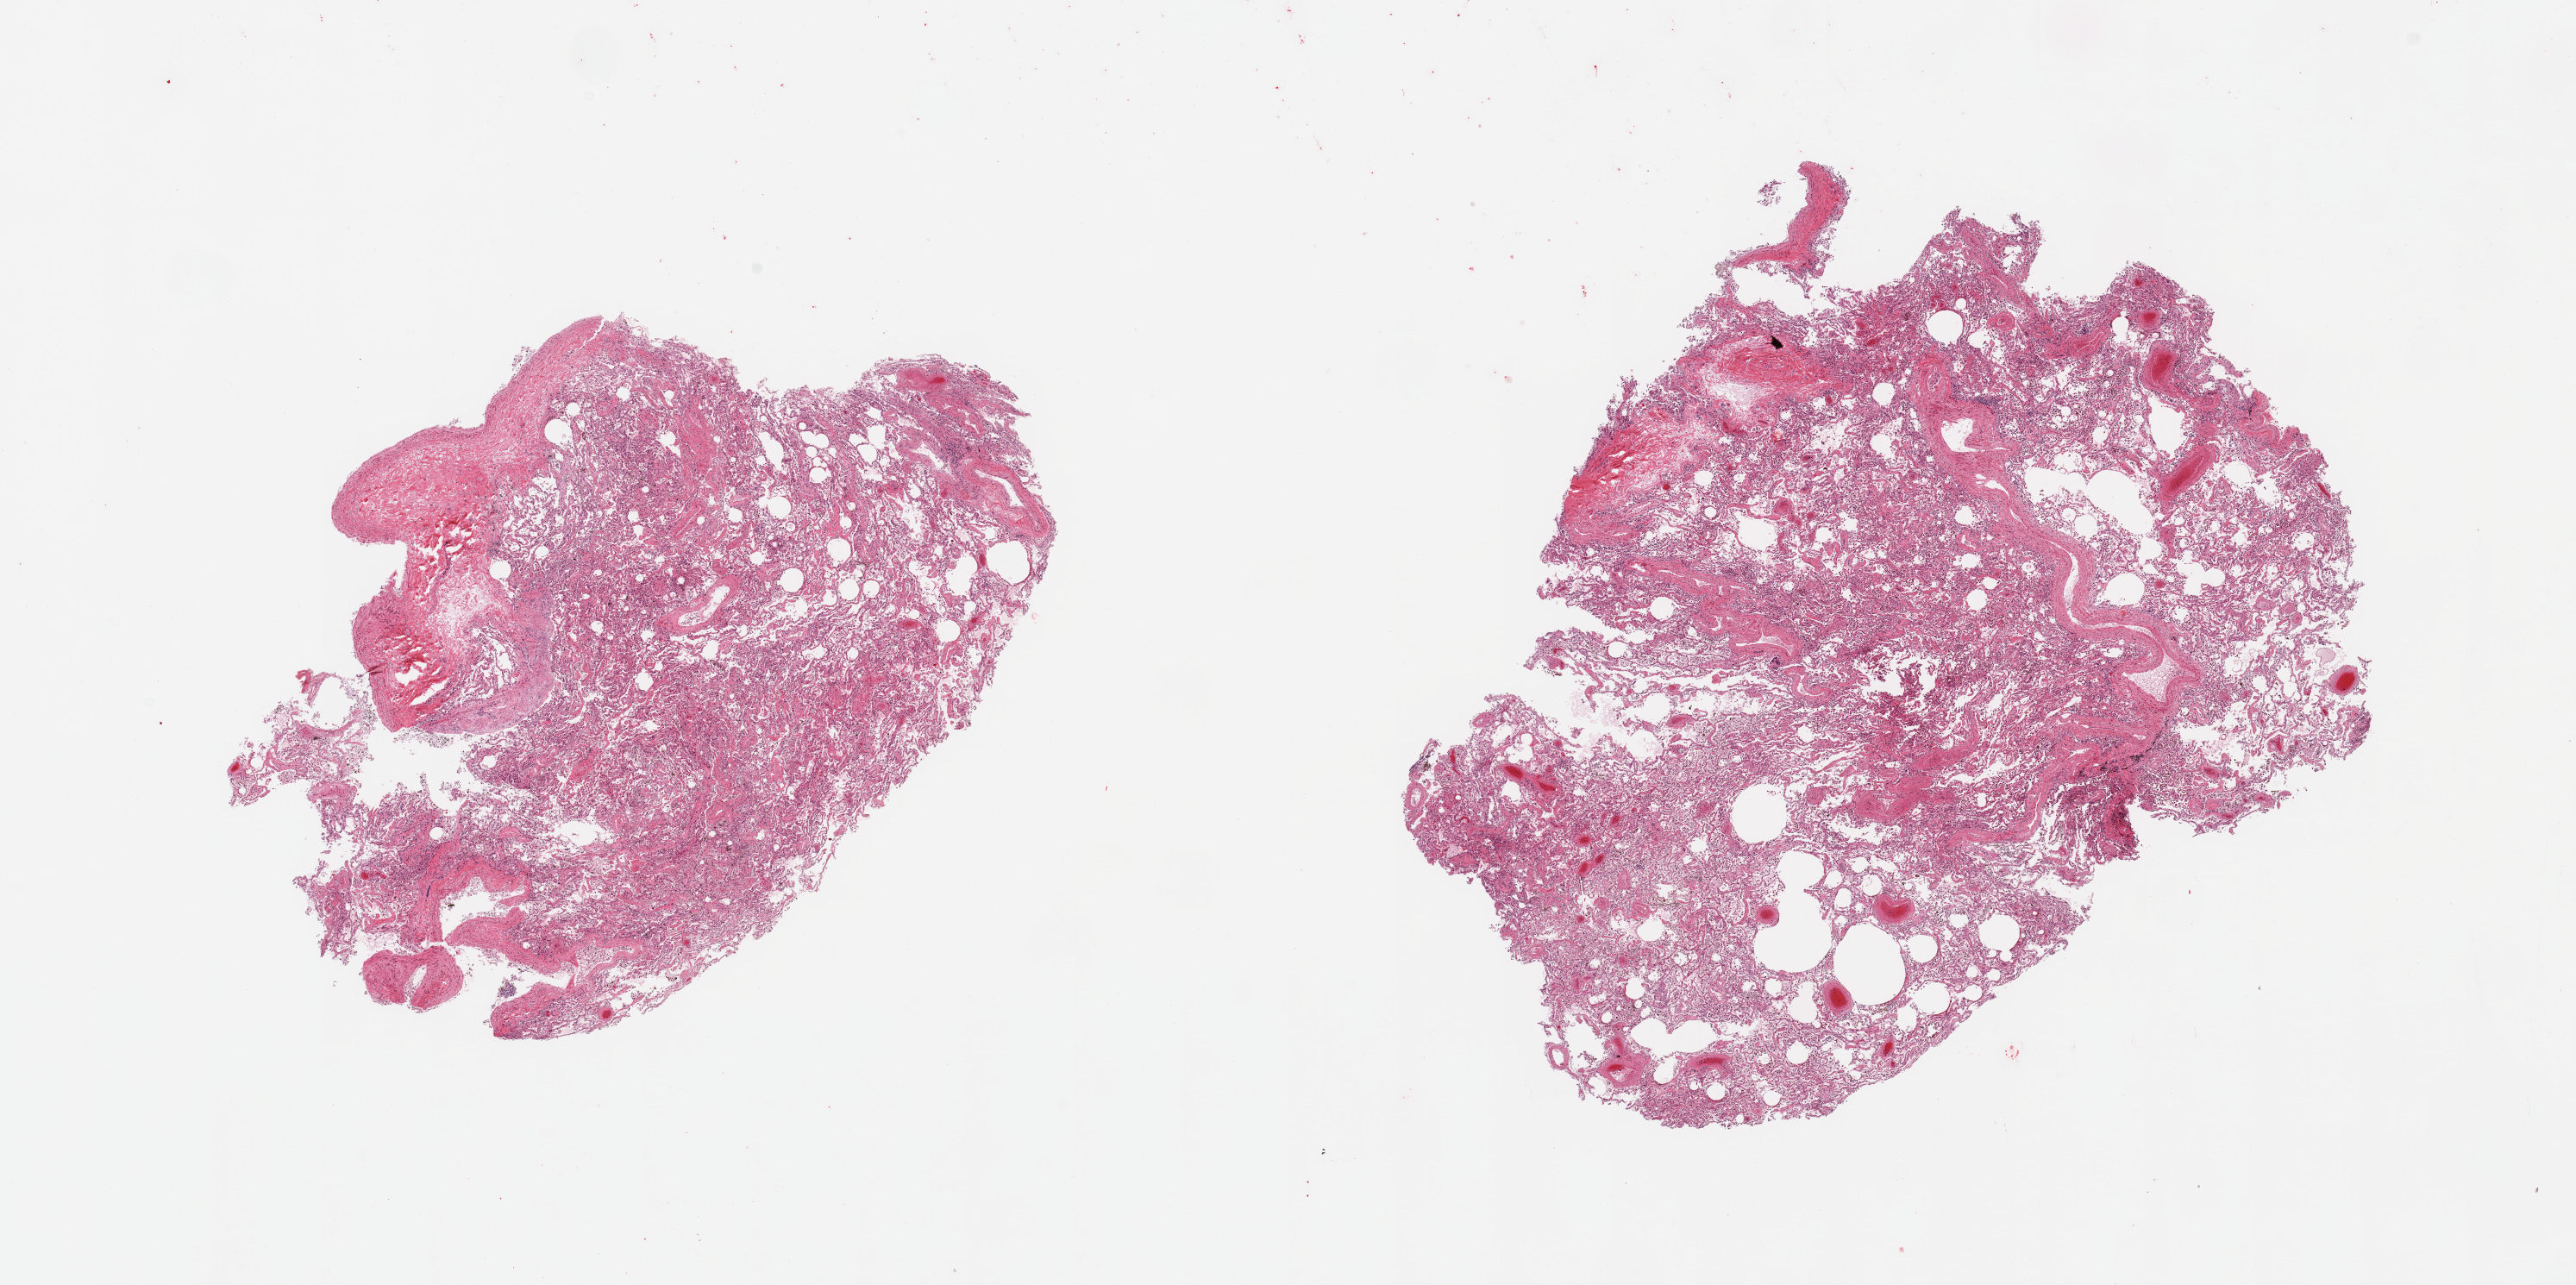
Digitized haematoxylin and eosin-stained section, low-resolution overview of the scanned area, about 23.6 x 11.8 mm (slide scanned at 20x), PAXgene-fixed paraffin-embedded (PFPE) section, target tissue: lung, tissue donor sample. Donor sex: male.
Review note (as recorded): 2 pieces, moderate congestion.